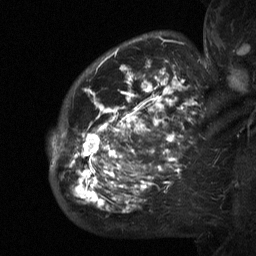
Breast MRI (dynamic contrast-enhanced), one sagittal slice. Slice 46 of 64 in the series (ordered by position). Dynamic contrast-enhanced study with each time point stored as its own series, time point 2 of 3 at this slice position (early post-contrast, ordered by acquisition time). 1.5 T. TE 4.8 ms, TR 27 ms. 2.3 mm slice thickness. 256 × 256 image matrix, field of view 200 × 200 mm. Patient: female, 50 years. From the clinical record (not read from this slice): setting: breast cancer imaged before/during neoadjuvant chemotherapy; receptor status: HER2-positive.
Outlined on this slice (semi-automatically segmented with operator editing):
- analysis volume of interest (the breast-tissue region the enhancement analysis was run in; not a lesion): bounding box [x1, y1, x2, y2] px = [53, 64, 211, 218]
- tumour enhancement mask (voxels above the 90 % enhancement threshold inside the analysis volume of interest): [53, 64, 200, 213]